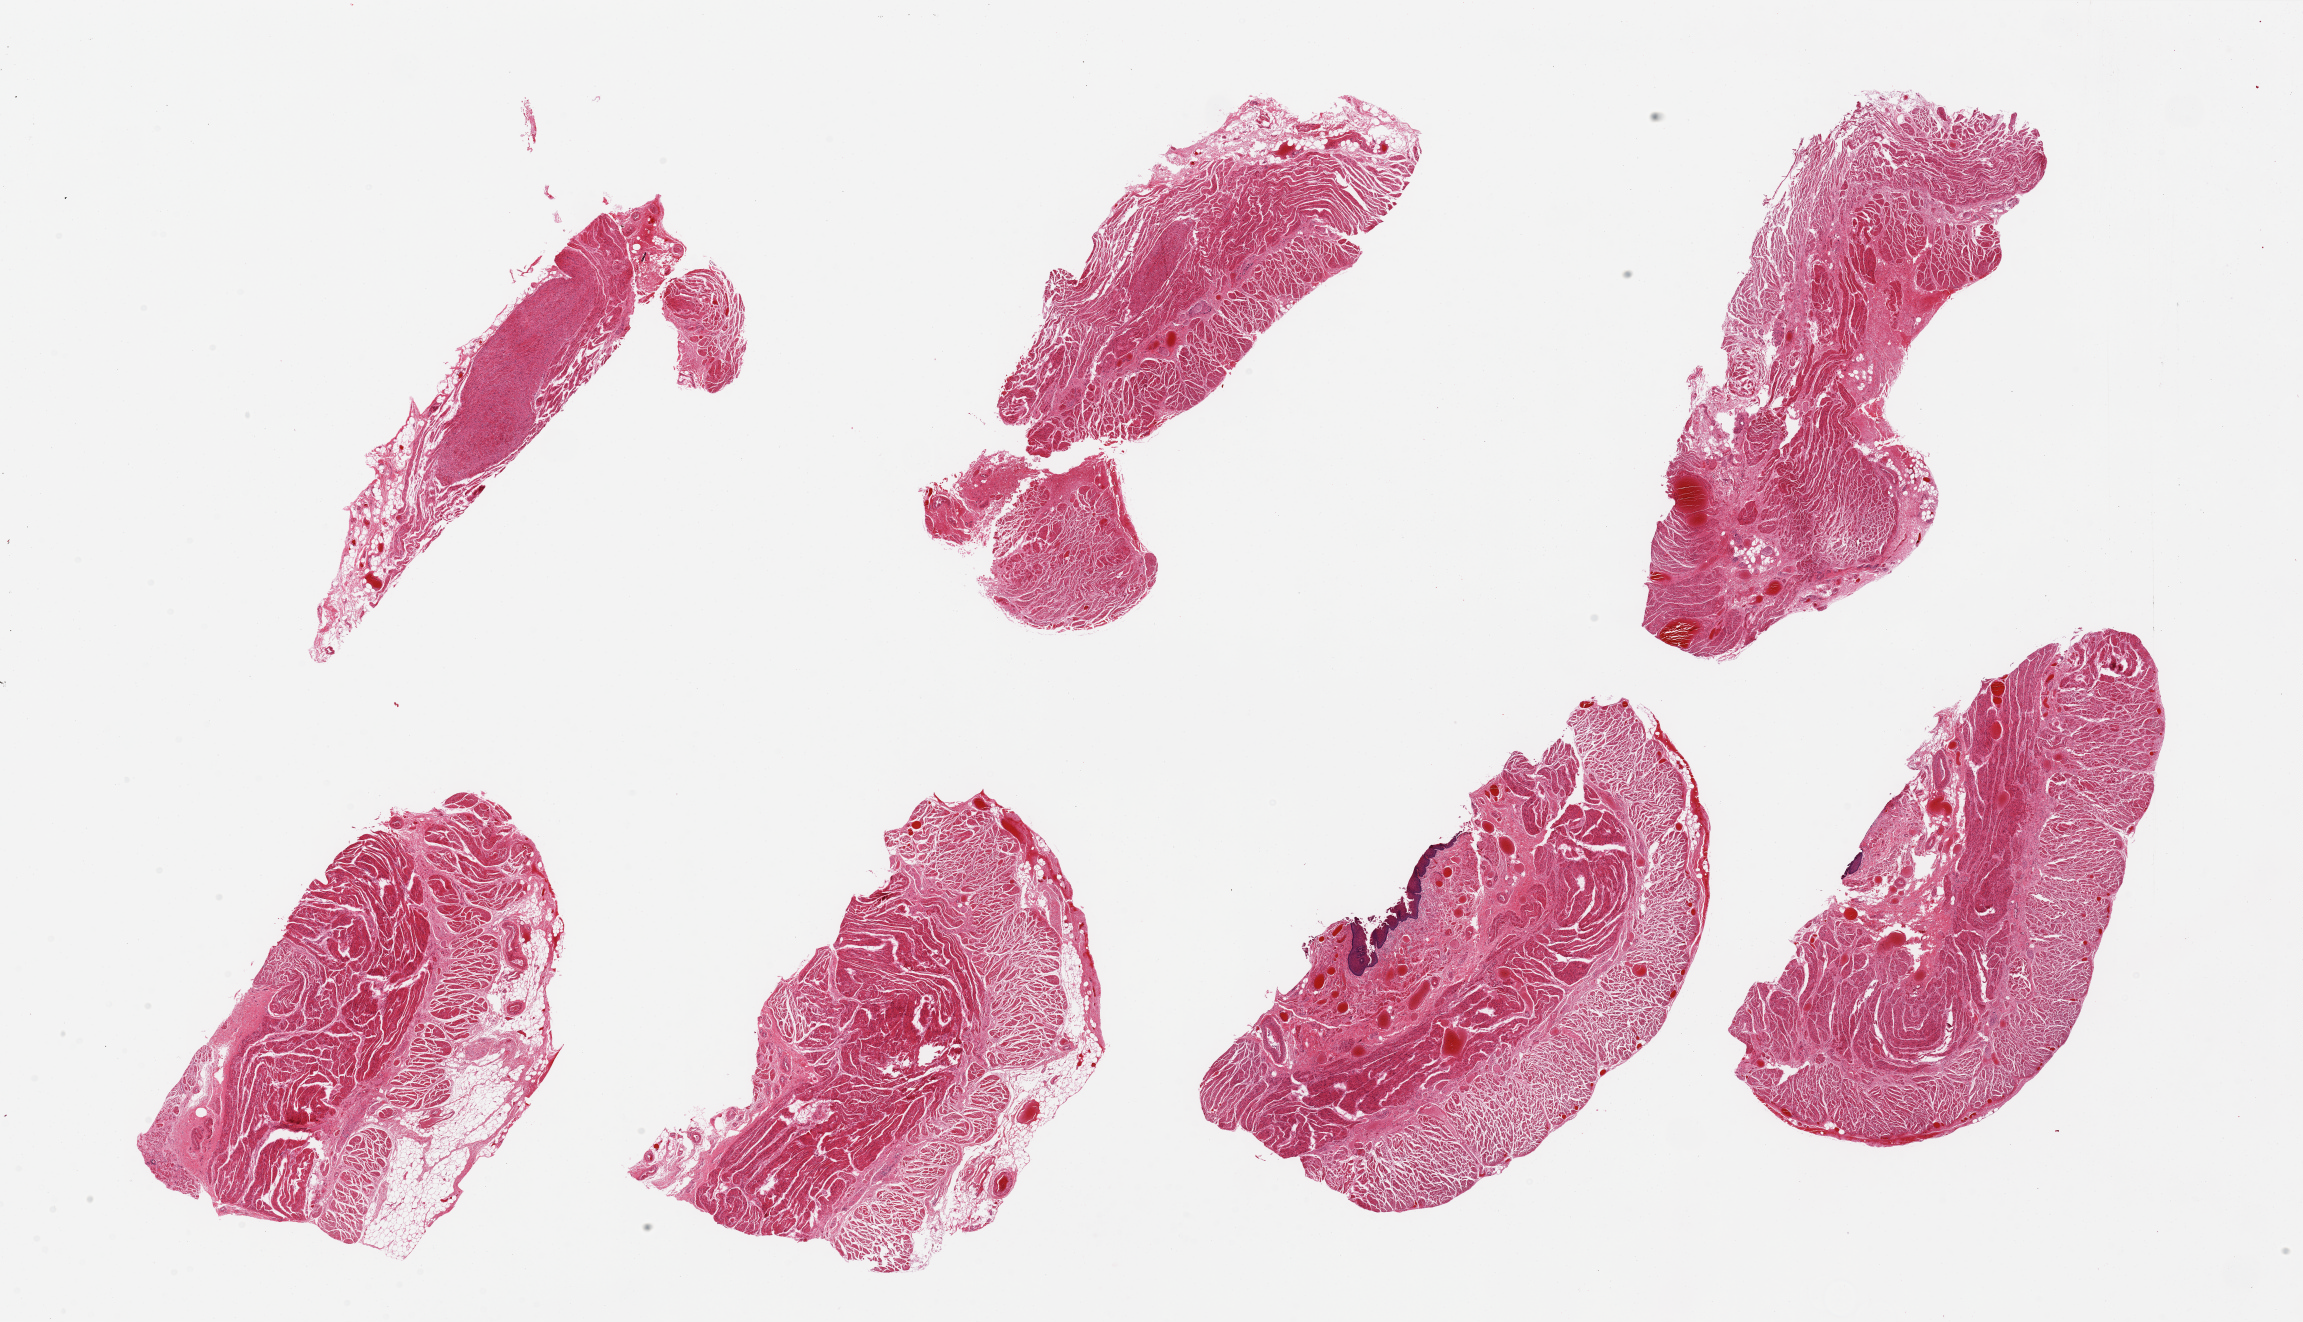
Digitized haematoxylin and eosin-stained section, brightfield — whole scanned area (about 36.4 x 20.9 mm, slide scanned at 20x) shown as a low-resolution overview. PAXgene-fixed paraffin-embedded (PFPE) section. Section of gastroesophageal junction (target tissue). Tissue donor sample. Donor: male.
• reviewer comment on this tissue sample: 7 pieces, predominantly muscularis, with few small strip of squamous mucosa